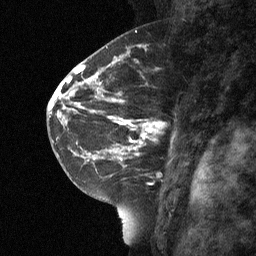
Breast MRI (dynamic contrast-enhanced), one sagittal slice. Slice 38 of 64 in the series (ordered by position). Dynamic contrast-enhanced study with each time point stored as its own series, time point 2 of 3 at this slice position (early post-contrast, ordered by acquisition time). 1.5 T. TE 4.8 ms, TR 27 ms. 2 mm slice thickness. 256 × 256 image matrix, field of view 180 × 180 mm. Female patient, age 42 years. From the clinical record (not read from this slice): setting: breast cancer imaged before/during neoadjuvant chemotherapy; receptor status: triple-negative.
Annotated regions visible in this slice (semi-automatically segmented with operator editing):
- analysis volume of interest (the breast-tissue region the enhancement analysis was run in; not a lesion): bounding box <115,90,186,160> (left, top, right, bottom; pixels)
- tumour enhancement mask (voxels above the 90 % enhancement threshold inside the analysis volume of interest): <115,98,145,160>